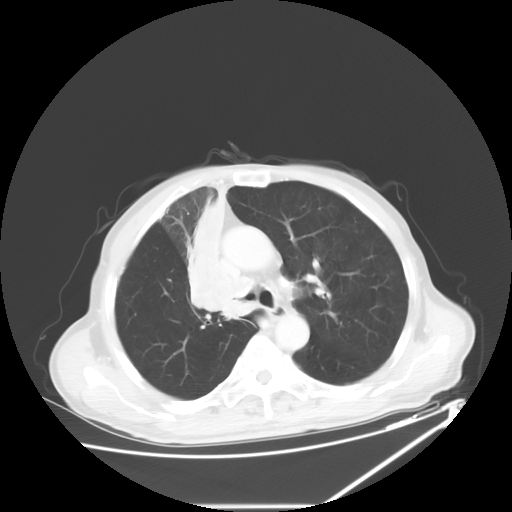
Chest CT, one axial slice. Position 42 of 60 along the scan axis. Reconstruction kernel STANDARD. 120 kVp. Lung window (W 1500 / L -600 HU). 5 mm slice thickness. 512 × 512 image matrix, field of view 410 × 410 mm. Patient: male, 73 years. From the clinical record (not read from this slice): clinical TNM (as recorded): T2a N1 M0.
Structures marked on this image (rectangle marked by the reading radiologist):
- lung tumour (recorded histology: squamous cell carcinoma): bounding box (x1, y1, x2, y2) in pixels: (178, 192, 254, 324)